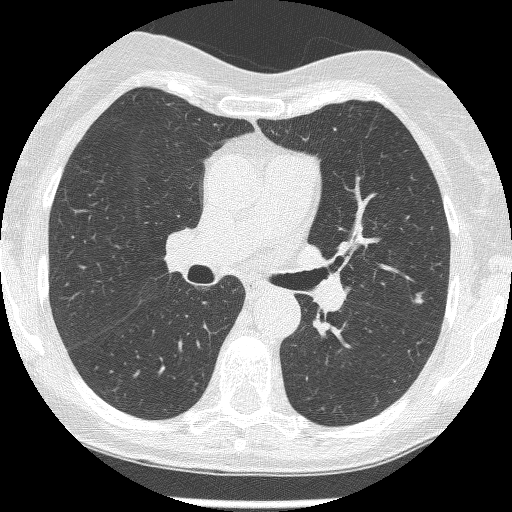
Axial slice from a low-dose chest CT screening exam, second screening round (one year after baseline), lung window (W 1500 / L -600 HU), 1.25 mm slice thickness. Female, age 60 years at enrolment. Current smoker at enrolment.
• Expert-annotated lung lesion, bounding box <401,286,438,315> (left, top, right, bottom; pixels).
• The screening reader recorded 2 non-calcified nodules or masses ≥4 mm on this exam; which of them this box marks is not recorded.
• Official screen result: positive, change unspecified: nodule(s) >= 4 mm or enlarging nodule(s), mass(es), or other non-specific abnormalities suspicious for lung cancer.